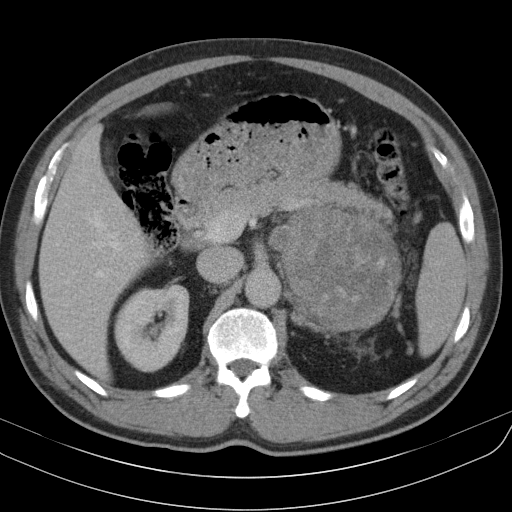
Contrast-enhanced abdominal CT, one axial slice. Slice 67 of 91 in the series (ordered by position). Reconstruction kernel B31s. Intravenous contrast given. Soft-tissue window (W 400 / L 40 HU). 5 mm slice thickness. 512 × 512 image matrix, field of view 370 × 370 mm. Patient: male, 51 years. Case-level facts recorded for this patient, not image findings: diagnosis: adrenocortical carcinoma; tumour side: left adrenal.
Annotated regions visible in this slice (semi-automatically segmented with operator editing):
- mass: box from (x=269, y=209) to (x=399, y=329) px